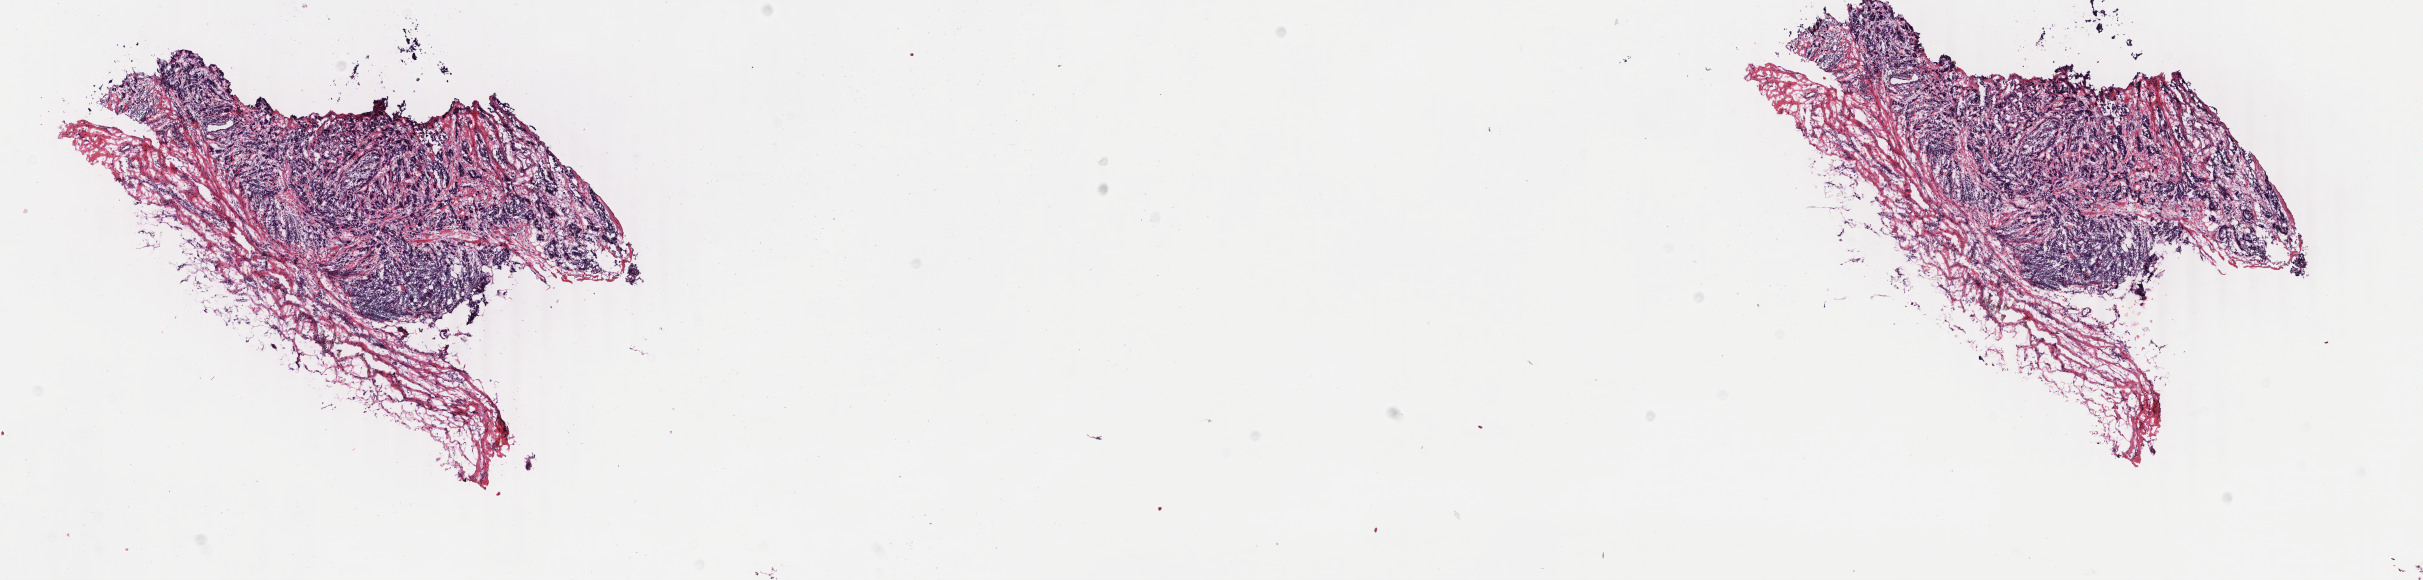
Whole-slide histology image, H&E-stained, low-resolution overview of the scanned area, about 19.3 x 4.6 mm; frozen section from the bottom of the tissue portion; breast, primary tumour sample. Female patient; age at initial diagnosis 49 years. Pathologist review of this section (percent, as recorded): tumour cells 75%, tumour nuclei 75%, normal cells 1%, stromal cells 24%, necrosis 0%. Inflammatory infiltration, as recorded: lymphocyte infiltration 6%, monocyte infiltration 0%, neutrophil infiltration 0%.
* AJCC pathologic stage: IIIA
* pathologic diagnosis: Infiltrating duct mixed with other types of carcinoma
* laterality: right
* lymph nodes positive (case pathology): 4 of 19 examined